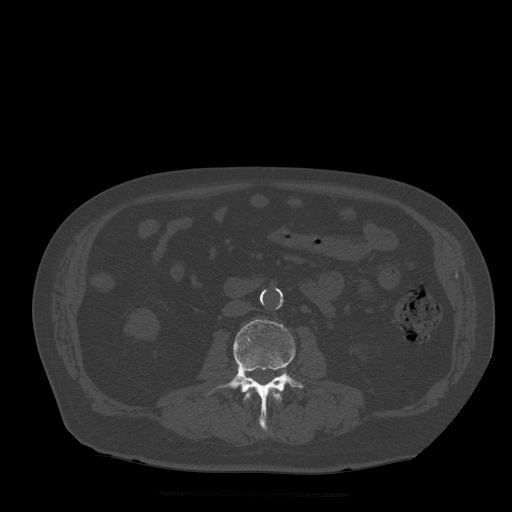
CT including the spine, one axial slice. Slice 142 of 522 in the series (ordered by position). Bone window (W 1800 / L 400 HU). 1.25 mm slice thickness. 512 × 512 image matrix, field of view 420 × 420 mm. Patient age 72 years. From the clinical record (not read from this slice): primary cancer: prostate.
Structures marked on this image (semi-automatically segmented with operator editing):
- L2 vertebra: bounding box [x1, y1, x2, y2] px = [244, 381, 282, 425]
- L3 vertebra: [208, 320, 305, 430]